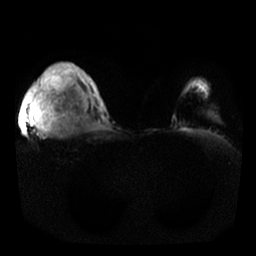
Breast MRI, one axial slice; slice 21 of 25 in the series (ordered by position); diffusion-weighted series; image 2 of 4 stored at this slice position (different b-values; order by instance number); 1.5 T; 256 × 256 image matrix, field of view 350 × 350 mm. Female patient.
Outlined on this slice (manually delineated by an expert):
- tumour on diffusion-weighted imaging: bounding box [x1, y1, x2, y2] px = [31, 63, 60, 133]